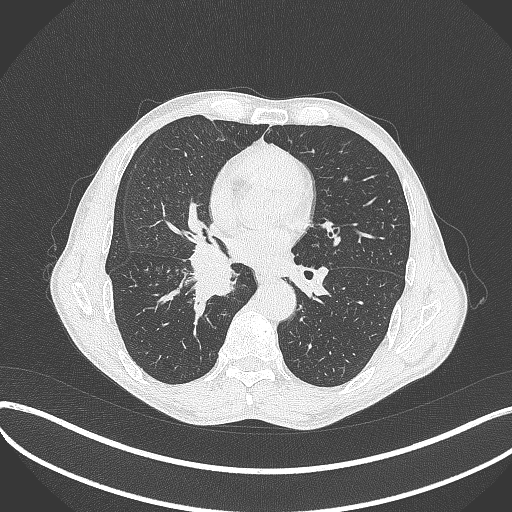
Chest CT, one axial slice. Slice 211 of 481 in the series (ordered by position). Reconstruction kernel B70f. 120 kVp. Lung window (W 1500 / L -600 HU). 512 × 512 image matrix. Male patient, age 65 years. From the clinical record (not read from this slice): clinical TNM (as recorded): T2a N0 M0; histopathological grade: G2.
Outlined on this slice (bounding box drawn by a radiologist):
- lung tumour (recorded histology: squamous cell carcinoma): box from (x=186, y=246) to (x=236, y=302) px